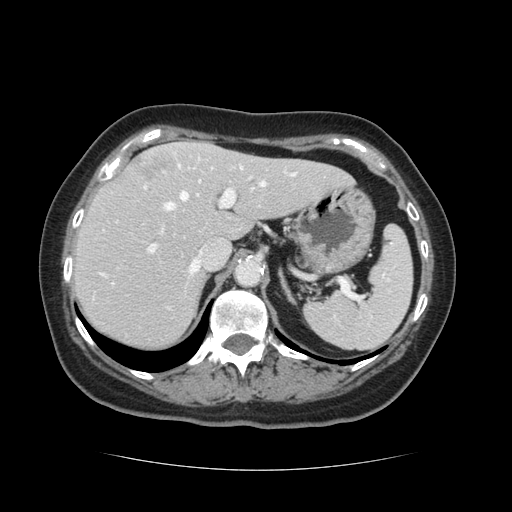
Contrast-enhanced abdominal CT, one axial slice. Slice 88 of 128 in the series (ordered by position). 120 kVp. Soft-tissue window (W 400 / L 40 HU). 2.5 mm slice thickness. 512 × 512 image matrix, field of view 366 × 366 mm. Female patient, age 67 years. From the clinical record (not read from this slice): diagnosis: colorectal cancer liver metastases, imaged before liver resection; multiple liver metastases: yes; largest metastasis: 3 cm; disease in both lobes: yes.
Structures marked on this image (outlined manually by an expert reader):
- hepatic veins: bounding box (x1, y1, x2, y2) in pixels: (165, 167, 296, 274)
- liver: (72, 144, 350, 350)
- planned liver remnant (the part of the liver to remain after resection): (72, 158, 350, 350)
- portal vein (with intrahepatic branches): (150, 166, 252, 251)
- liver metastasis: (136, 158, 170, 180)